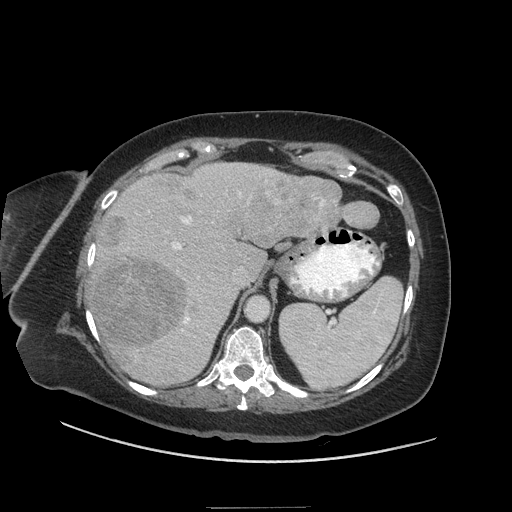
Contrast-enhanced abdominal CT (liver protocol), one axial slice; slice 39 of 81 in the series (ordered by position); reconstruction kernel STANDARD; 140 kVp; soft-tissue window (W 400 / L 40 HU); 2.5 mm slice thickness; 512 × 512 image matrix, field of view 440 × 440 mm. From the clinical record (not read from this slice): diagnosis: hepatocellular carcinoma (patient treated with transarterial chemoembolisation; whether this scan precedes or follows treatment is not stated here); TNM stage (as recorded): Stage-II; Child-Pugh class: A; tumour nodularity: multinodular.
Outlined on this slice (semi-automatically segmented with operator editing):
- liver parenchyma outside the tumour (the mass and vessels are separate outlines, so this box may not span the whole liver): bounding box [x1, y1, x2, y2] px = [88, 162, 340, 386]
- mass: [92, 173, 379, 385]
- liver vessels: [148, 173, 272, 337]